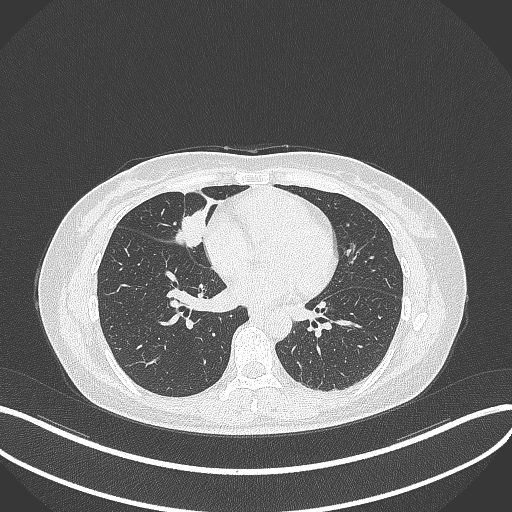
Chest CT, one axial slice. Position 120 of 284 along the scan axis. 120 kVp. Lung window (W 1500 / L -600 HU). 1 mm slice thickness. 512 × 512 image matrix, field of view 400 × 400 mm. Patient: female, 43 years. From the clinical record (not read from this slice): clinical TNM (as recorded): T1c N3 M1.
Outlined on this slice (bounding box drawn by a radiologist):
- lung tumour (recorded histology: adenocarcinoma): box from (x=173, y=210) to (x=210, y=250) px